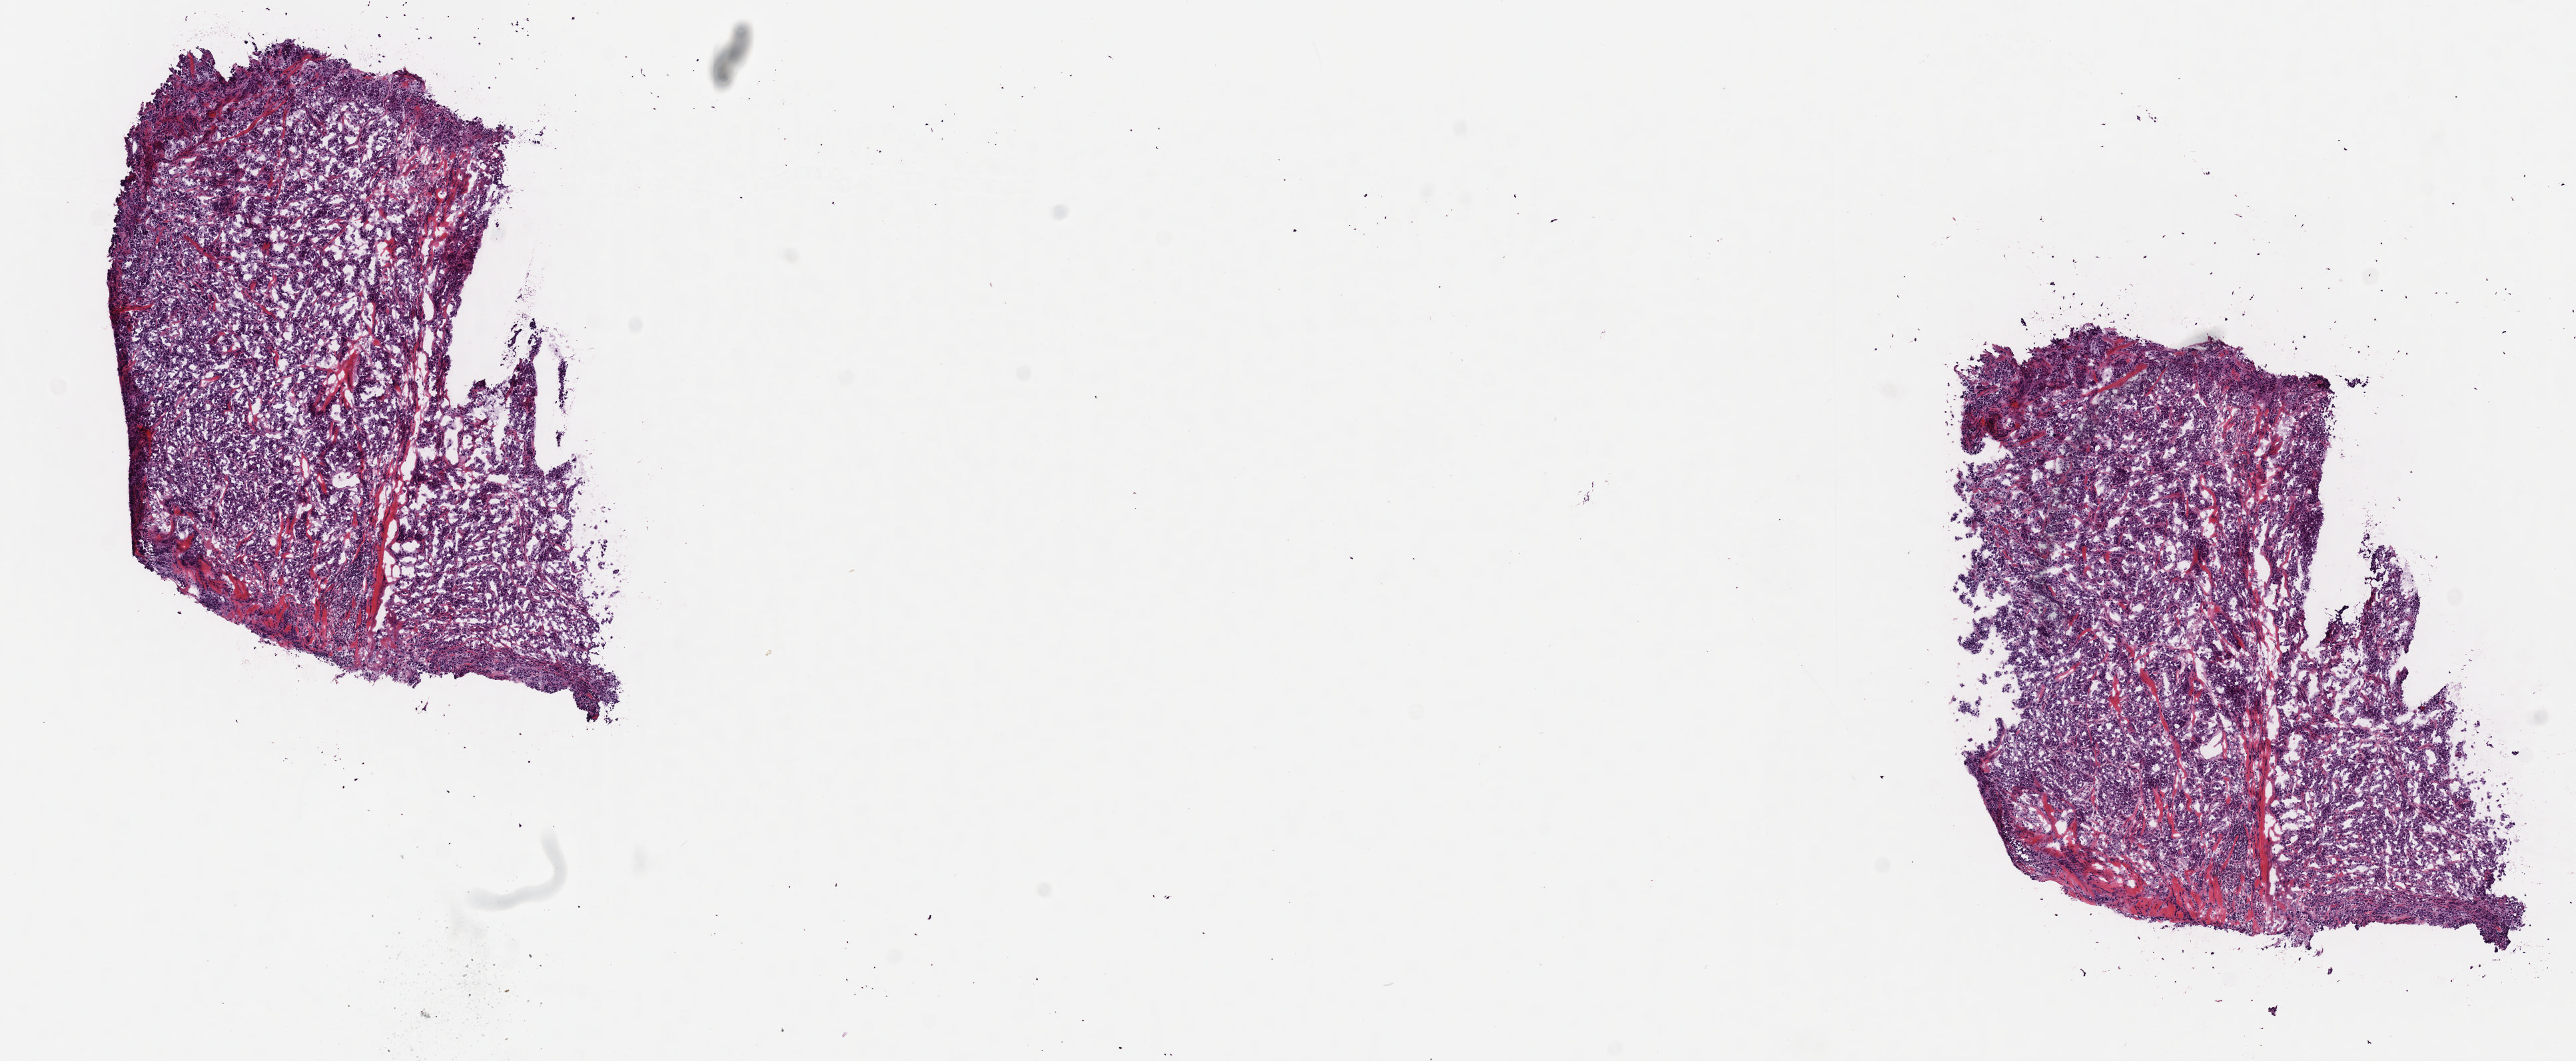
Digitized H&E-stained tissue section (whole slide), whole scanned area (about 15.3 x 6.3 mm) shown as a low-resolution overview. Frozen section from the top of the tissue portion. Metastatic tumour sample, sampled site not recorded. Patient: female, age at initial diagnosis 70 years. Composition of this section per pathologist review: tumour cells 85%, tumour nuclei 85%, normal cells 0%, stromal cells 15%, necrosis 0%. Inflammatory infiltration, as recorded: lymphocyte infiltration 1%, monocyte infiltration 1%, neutrophil infiltration 0%.
This section: metastatic tumour tissue. Patient diagnosis: Malignant melanoma, NOS.